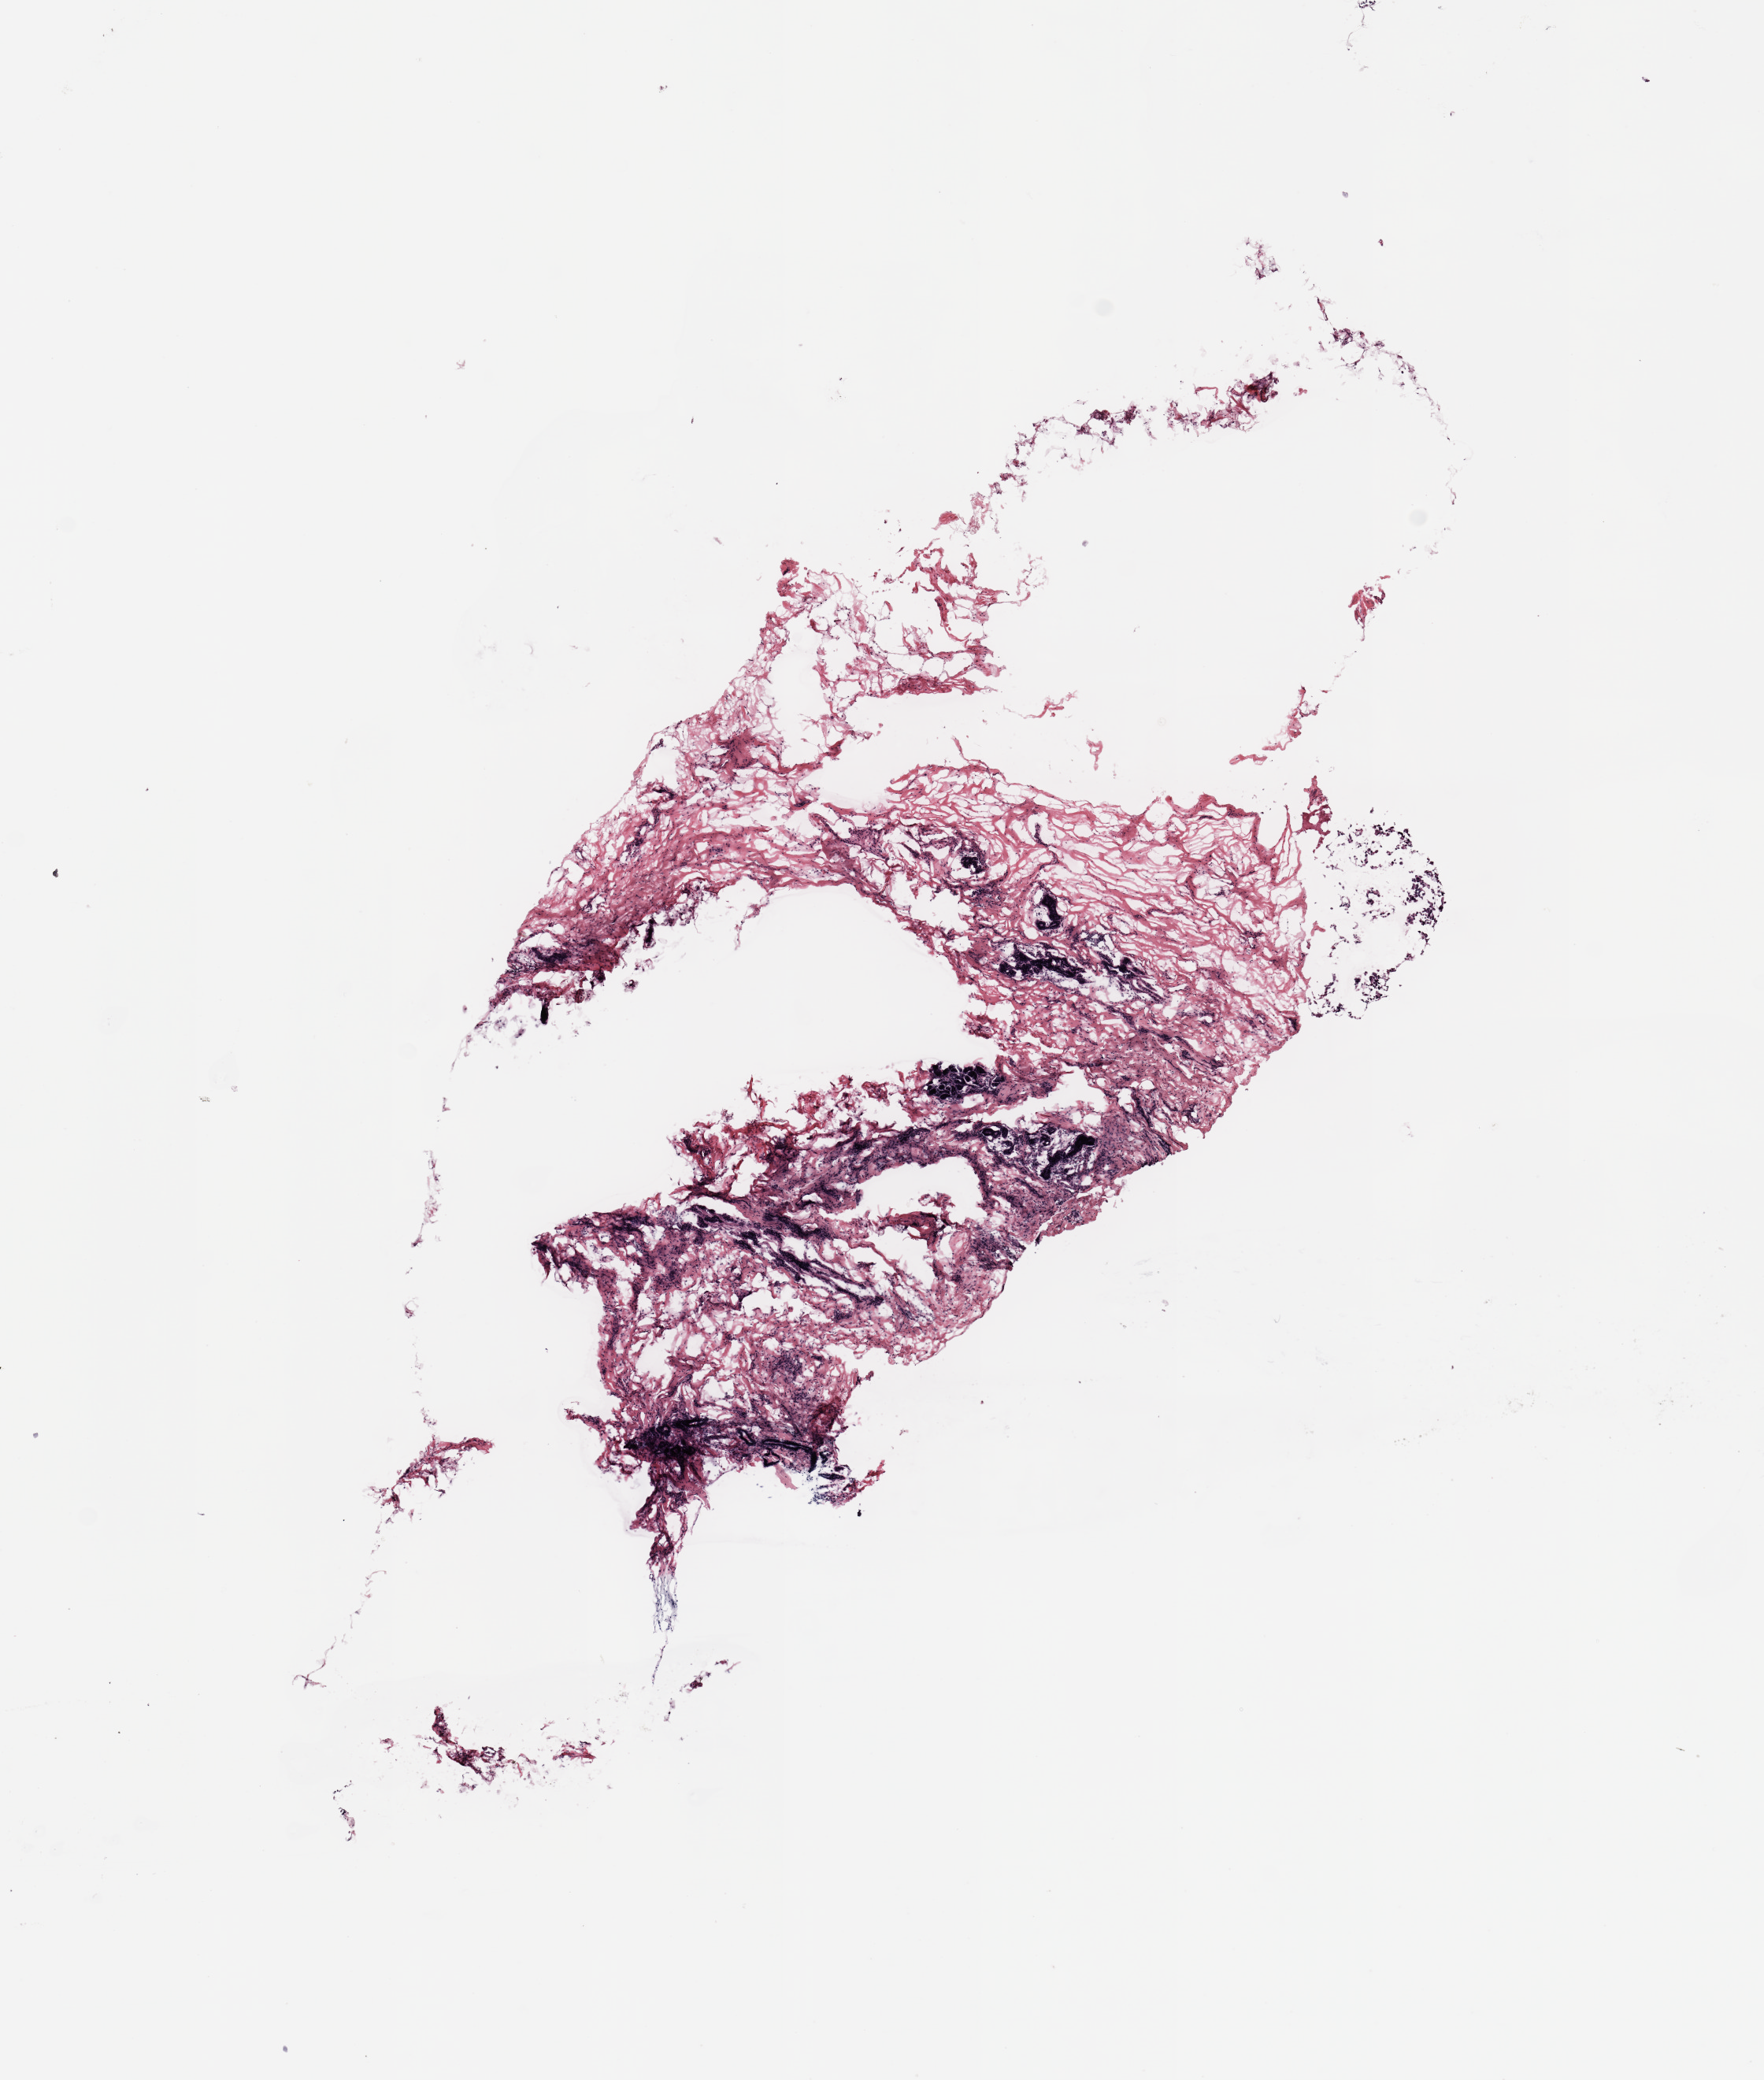
Whole-slide histology image, Hematoxylin and eosin (H&E) stained, shown as a low-resolution overview of the whole scanned area (about 8.9 x 10.4 mm, slide scanned at 20x); breast, tissue type not recorded. Female, 57 y/o.
Patient diagnosis: Infiltrating duct carcinoma, NOS.